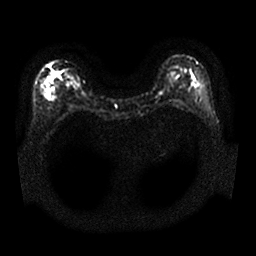
Breast MRI, one axial slice; slice 11 of 25 in the series (ordered by position); diffusion-weighted series; image 2 of 4 stored at this slice position (different b-values; order by instance number); 1.5 T; 256 × 256 image matrix. Female patient.
Structures marked on this image (outlined manually by an expert reader):
- tumour on diffusion-weighted imaging: bounding box <46,67,60,82> (left, top, right, bottom; pixels)